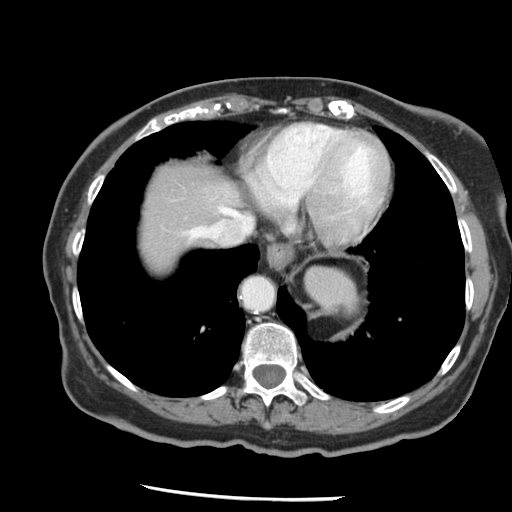
Contrast-enhanced abdominal CT, one axial slice. Slice 118 of 148 in the series (ordered by position). 120 kVp. Intravenous contrast given. Soft-tissue window (W 400 / L 40 HU). 2.5 mm slice thickness. 512 × 512 image matrix, field of view 330 × 330 mm. Female patient, age 85 years. From the clinical record (not read from this slice): diagnosis: colorectal cancer liver metastases, imaged before liver resection; multiple liver metastases: no; largest metastasis: 0.9 cm.
Annotated regions visible in this slice (manually delineated by an expert):
- hepatic veins: box from (x=183, y=207) to (x=252, y=243) px
- liver: (x=136, y=164)–(x=252, y=279)
- planned liver remnant (the part of the liver to remain after resection): (x=136, y=164)–(x=252, y=279)